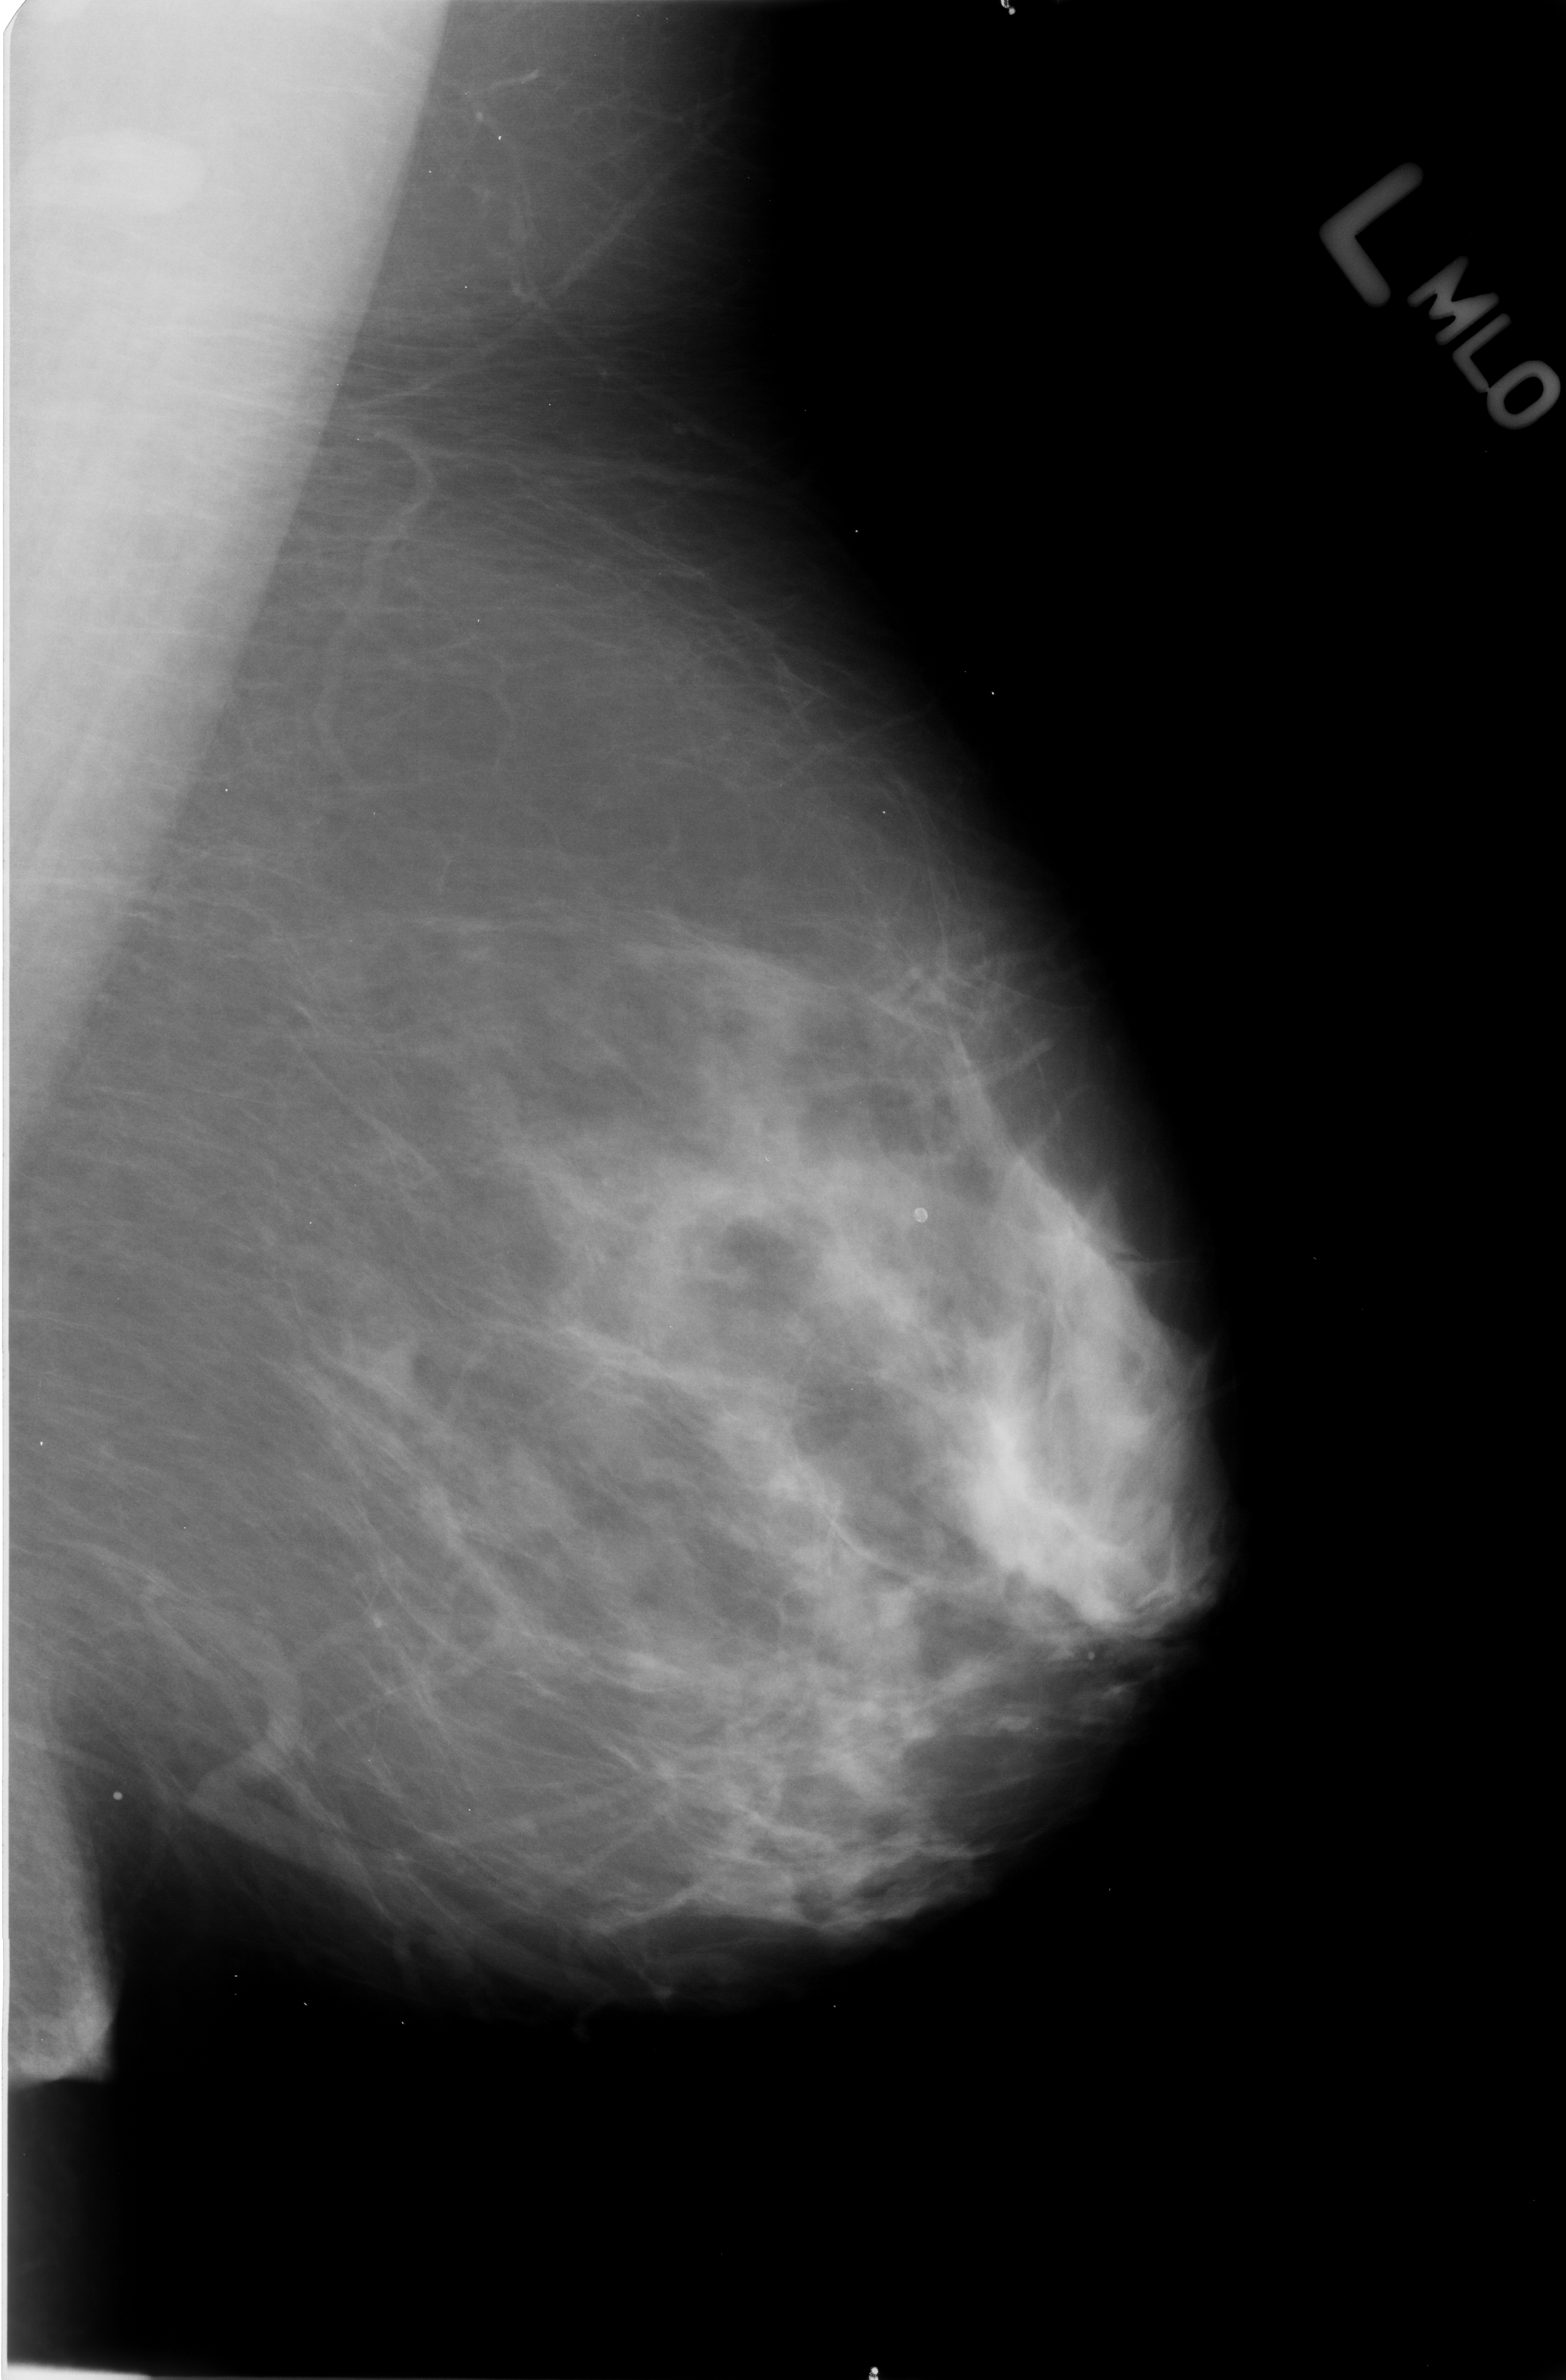
Mammogram (digitized film); left breast; mediolateral oblique (MLO) view; 1566 × 2380 image matrix.
Marked abnormalities (boxes around the expert regions of interest):
- calcifications, morphology lucent center; BI-RADS assessment category 2; subtlety rating 3 on a 1 (subtle) to 5 (obvious) scale; benign; no additional work-up was recommended (outcome (as recorded, no biopsy): benign without callback): bounding box (x1, y1, x2, y2) in pixels: (876, 1160, 974, 1262)